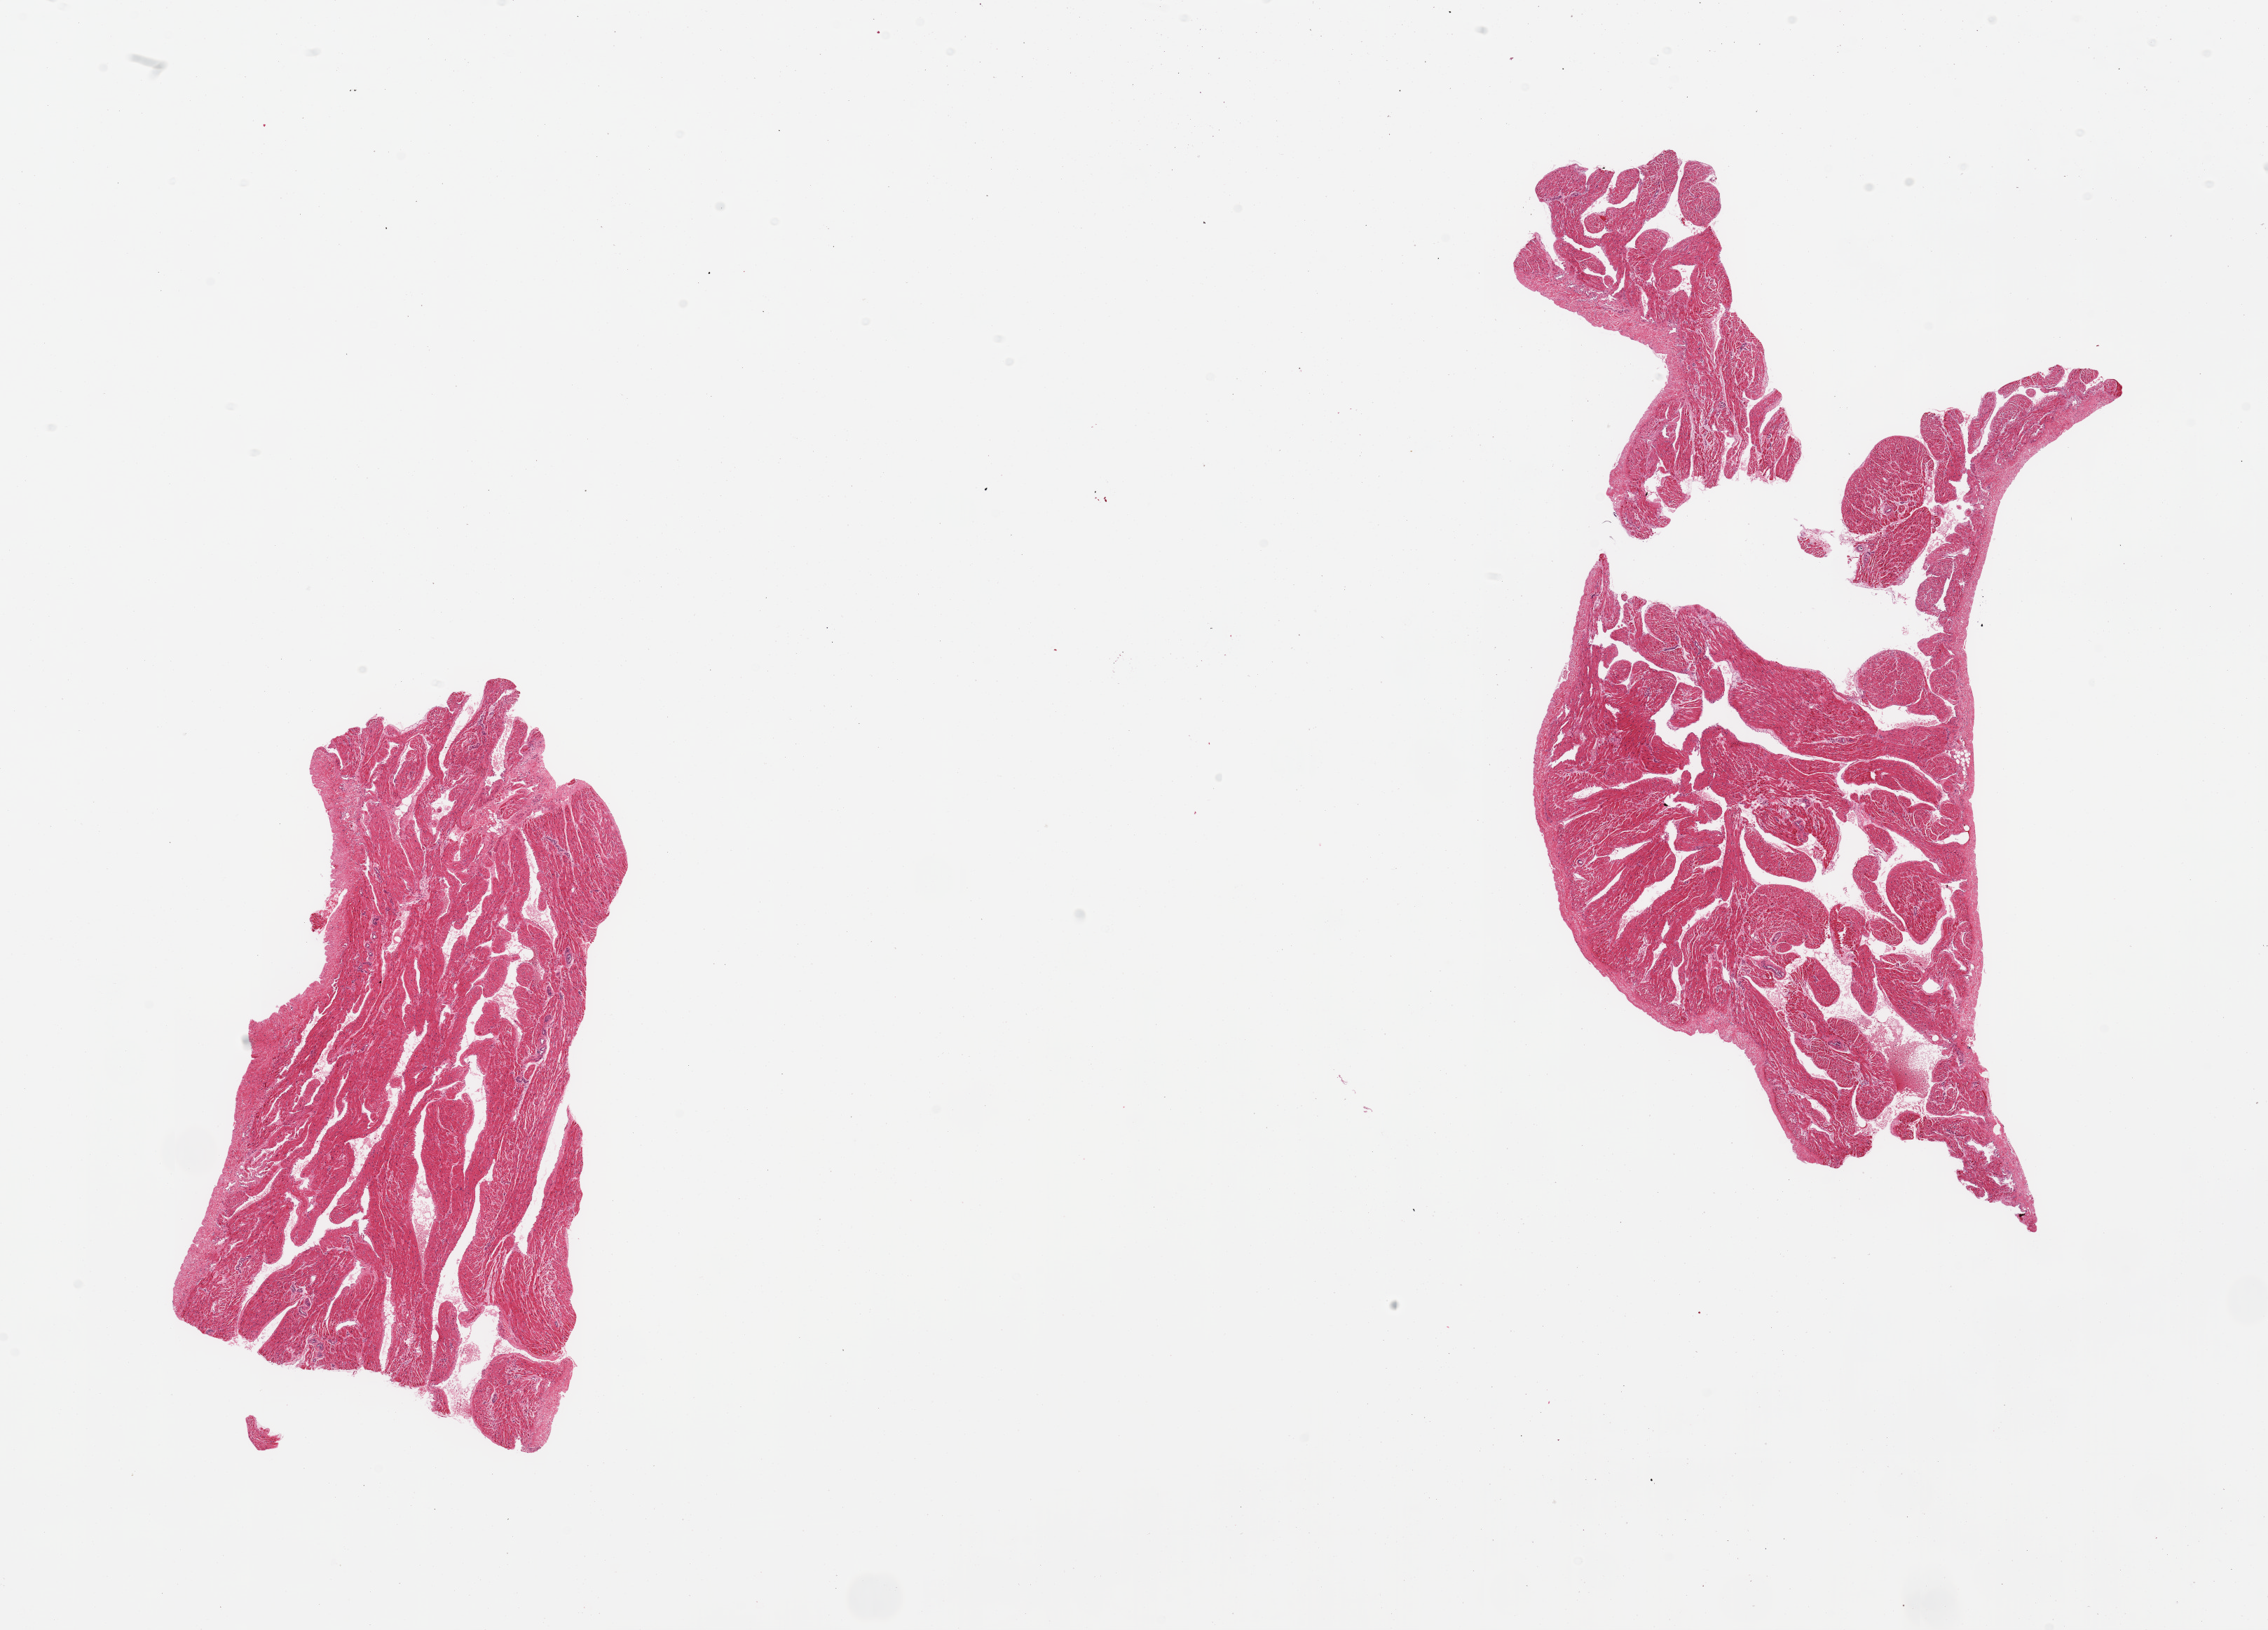
Digitized H&E-stained section, brightfield, shown as a low-resolution overview of the whole scanned area (about 25.6 x 18.4 mm); PAXgene-fixed, paraffin-embedded tissue; section of auricular appendage (target tissue); tissue donor sample.
Pathologist's review note for this sample: 2 pieces.